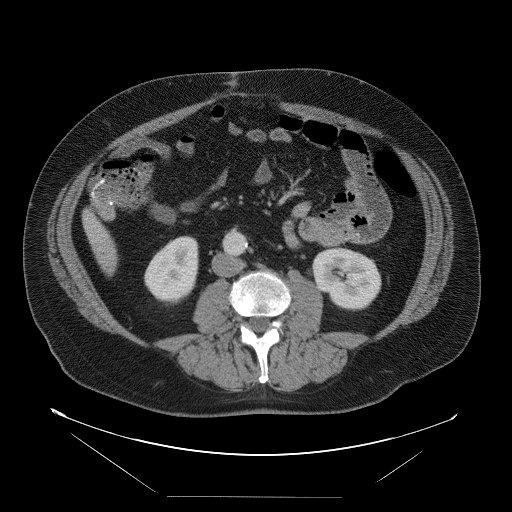
Contrast-enhanced abdominal CT, one axial slice. 120 kVp. Intravenous contrast given. Soft-tissue window (W 400 / L 40 HU). 5 mm slice thickness. 512 × 512 image matrix. Male patient, age 61 years. From the clinical record (not read from this slice): diagnosis: colorectal cancer liver metastases, imaged before liver resection.
Outlined on this slice (expert manual segmentation):
- liver: bounding box [x1, y1, x2, y2] px = [84, 211, 118, 273]